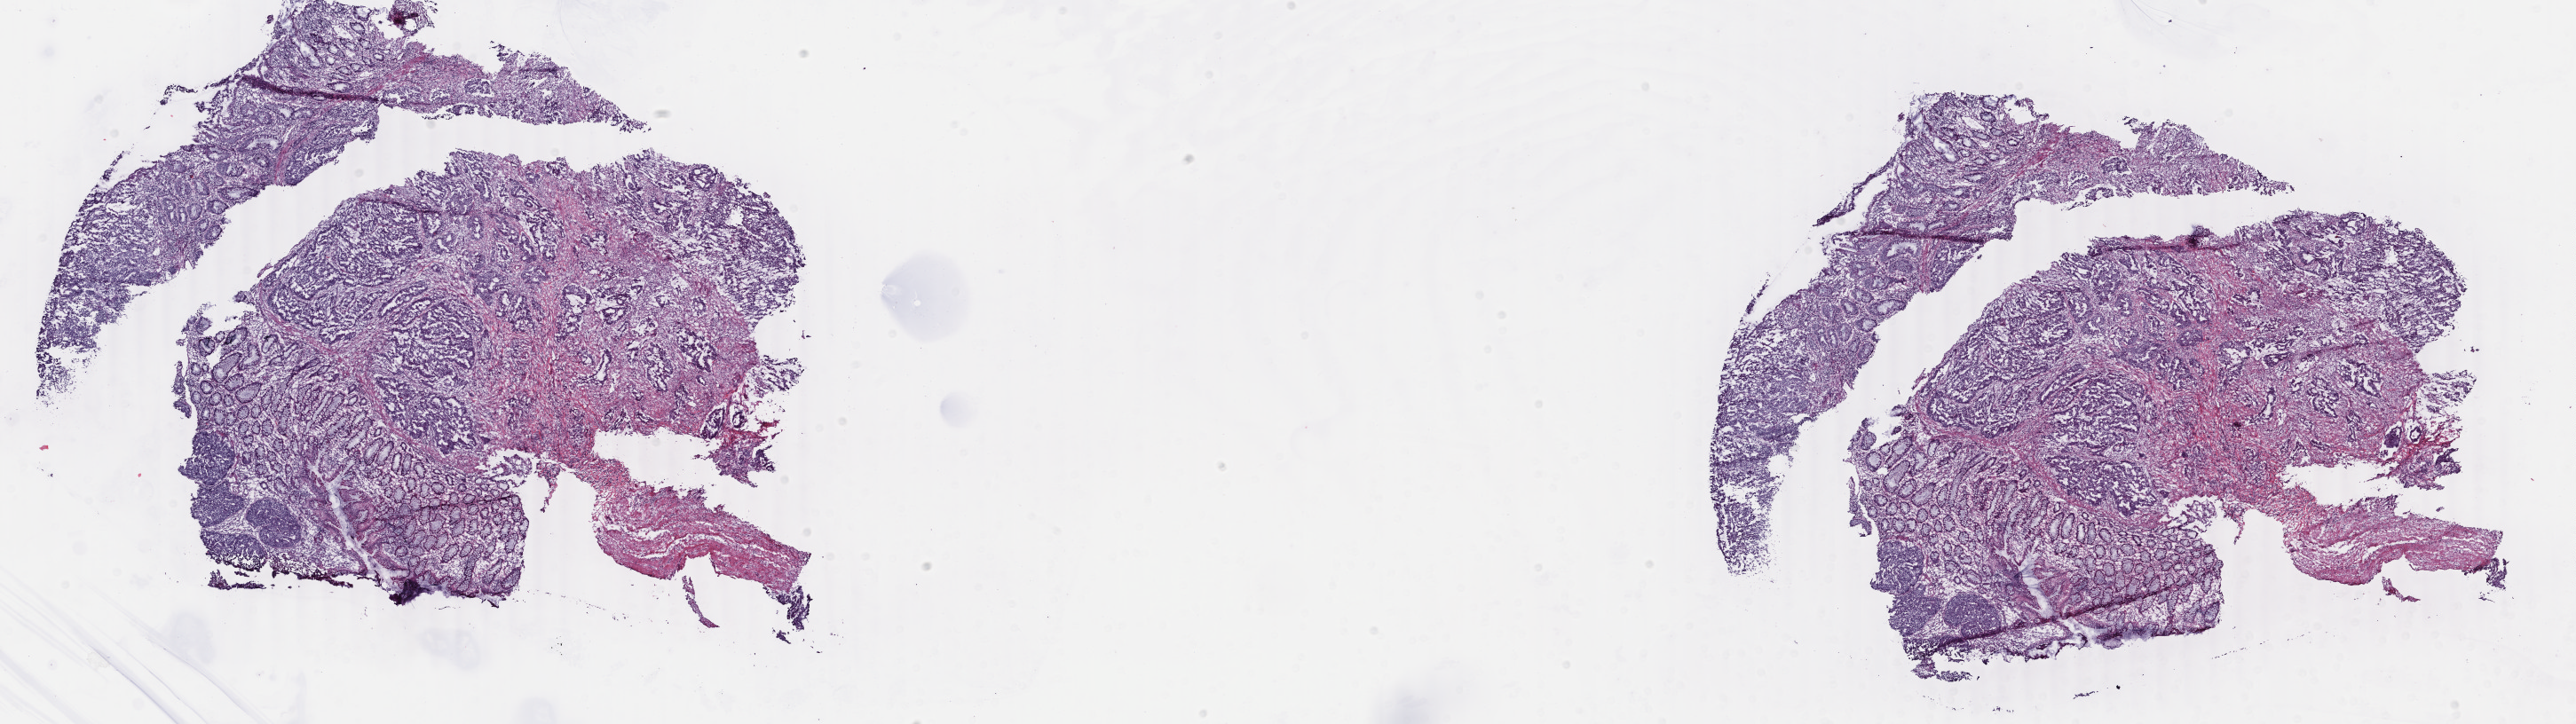
H&E whole-slide image — shown as a low-resolution overview of the whole scanned area (about 23.1 x 6.5 mm, from a 40x scan); frozen section; sample: primary tumour, rectum. Patient: female, age at initial diagnosis 62 years. Composition of this section per pathologist review: tumour cells 45%, tumour nuclei 65%, normal cells 45%, stromal cells 8%, necrosis 2%. Inflammatory infiltration, as recorded: lymphocyte infiltration 15%, monocyte infiltration 3%, neutrophil infiltration 5%.
AJCC pathologic stage: IV (5th edition). Pathologic diagnosis: Adenocarcinoma, NOS. Lymph nodes positive (case pathology): 6 of 12 examined.